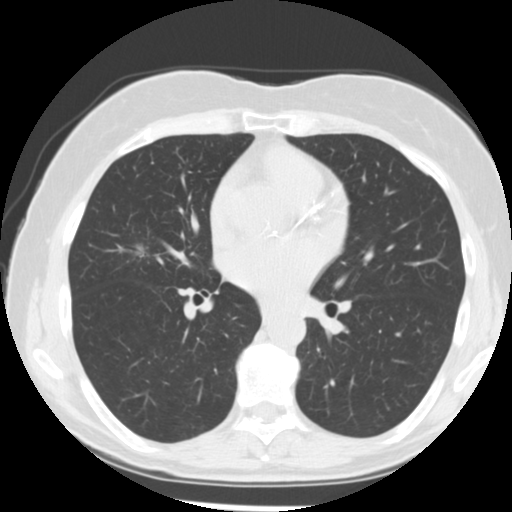
Low-dose screening chest CT, axial slice, first (baseline) screen, lung window (W 1500 / L -600 HU), slice 116 of 255 in the series. Female, age 66 years at enrolment. Former smoker at enrolment.
Expert-annotated lung lesion, bounding box (x1, y1, x2, y2) in pixels: (126, 240, 160, 271). Screening reader's record for this exam (one nodule recorded; not confirmed to be the boxed lesion): non-calcified nodule or mass ≥4 mm, right middle lobe, 15 × 13 mm, poorly defined margins, soft tissue attenuation. Lung cancer was diagnosed 27 days after this screen: adenocarcinoma, NOS, right middle lobe, undifferentiated (G4), stage IIIA (AJCC 6th edition), 18 mm at pathology.